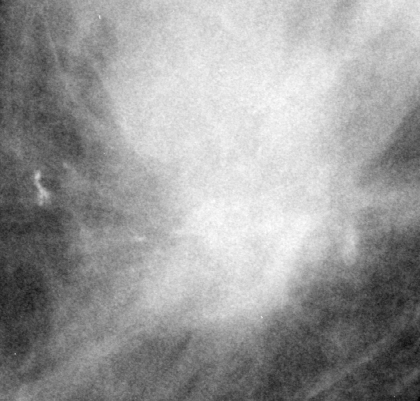
Cropped region of a digitized screen-film mammogram centred on a radiologist-marked abnormality, left breast, CC view, BI-RADS breast density category 3 (scale 1–4).
Mass, shape lobulated, margins spiculated; BI-RADS assessment category 5; pathology (as recorded): malignant.